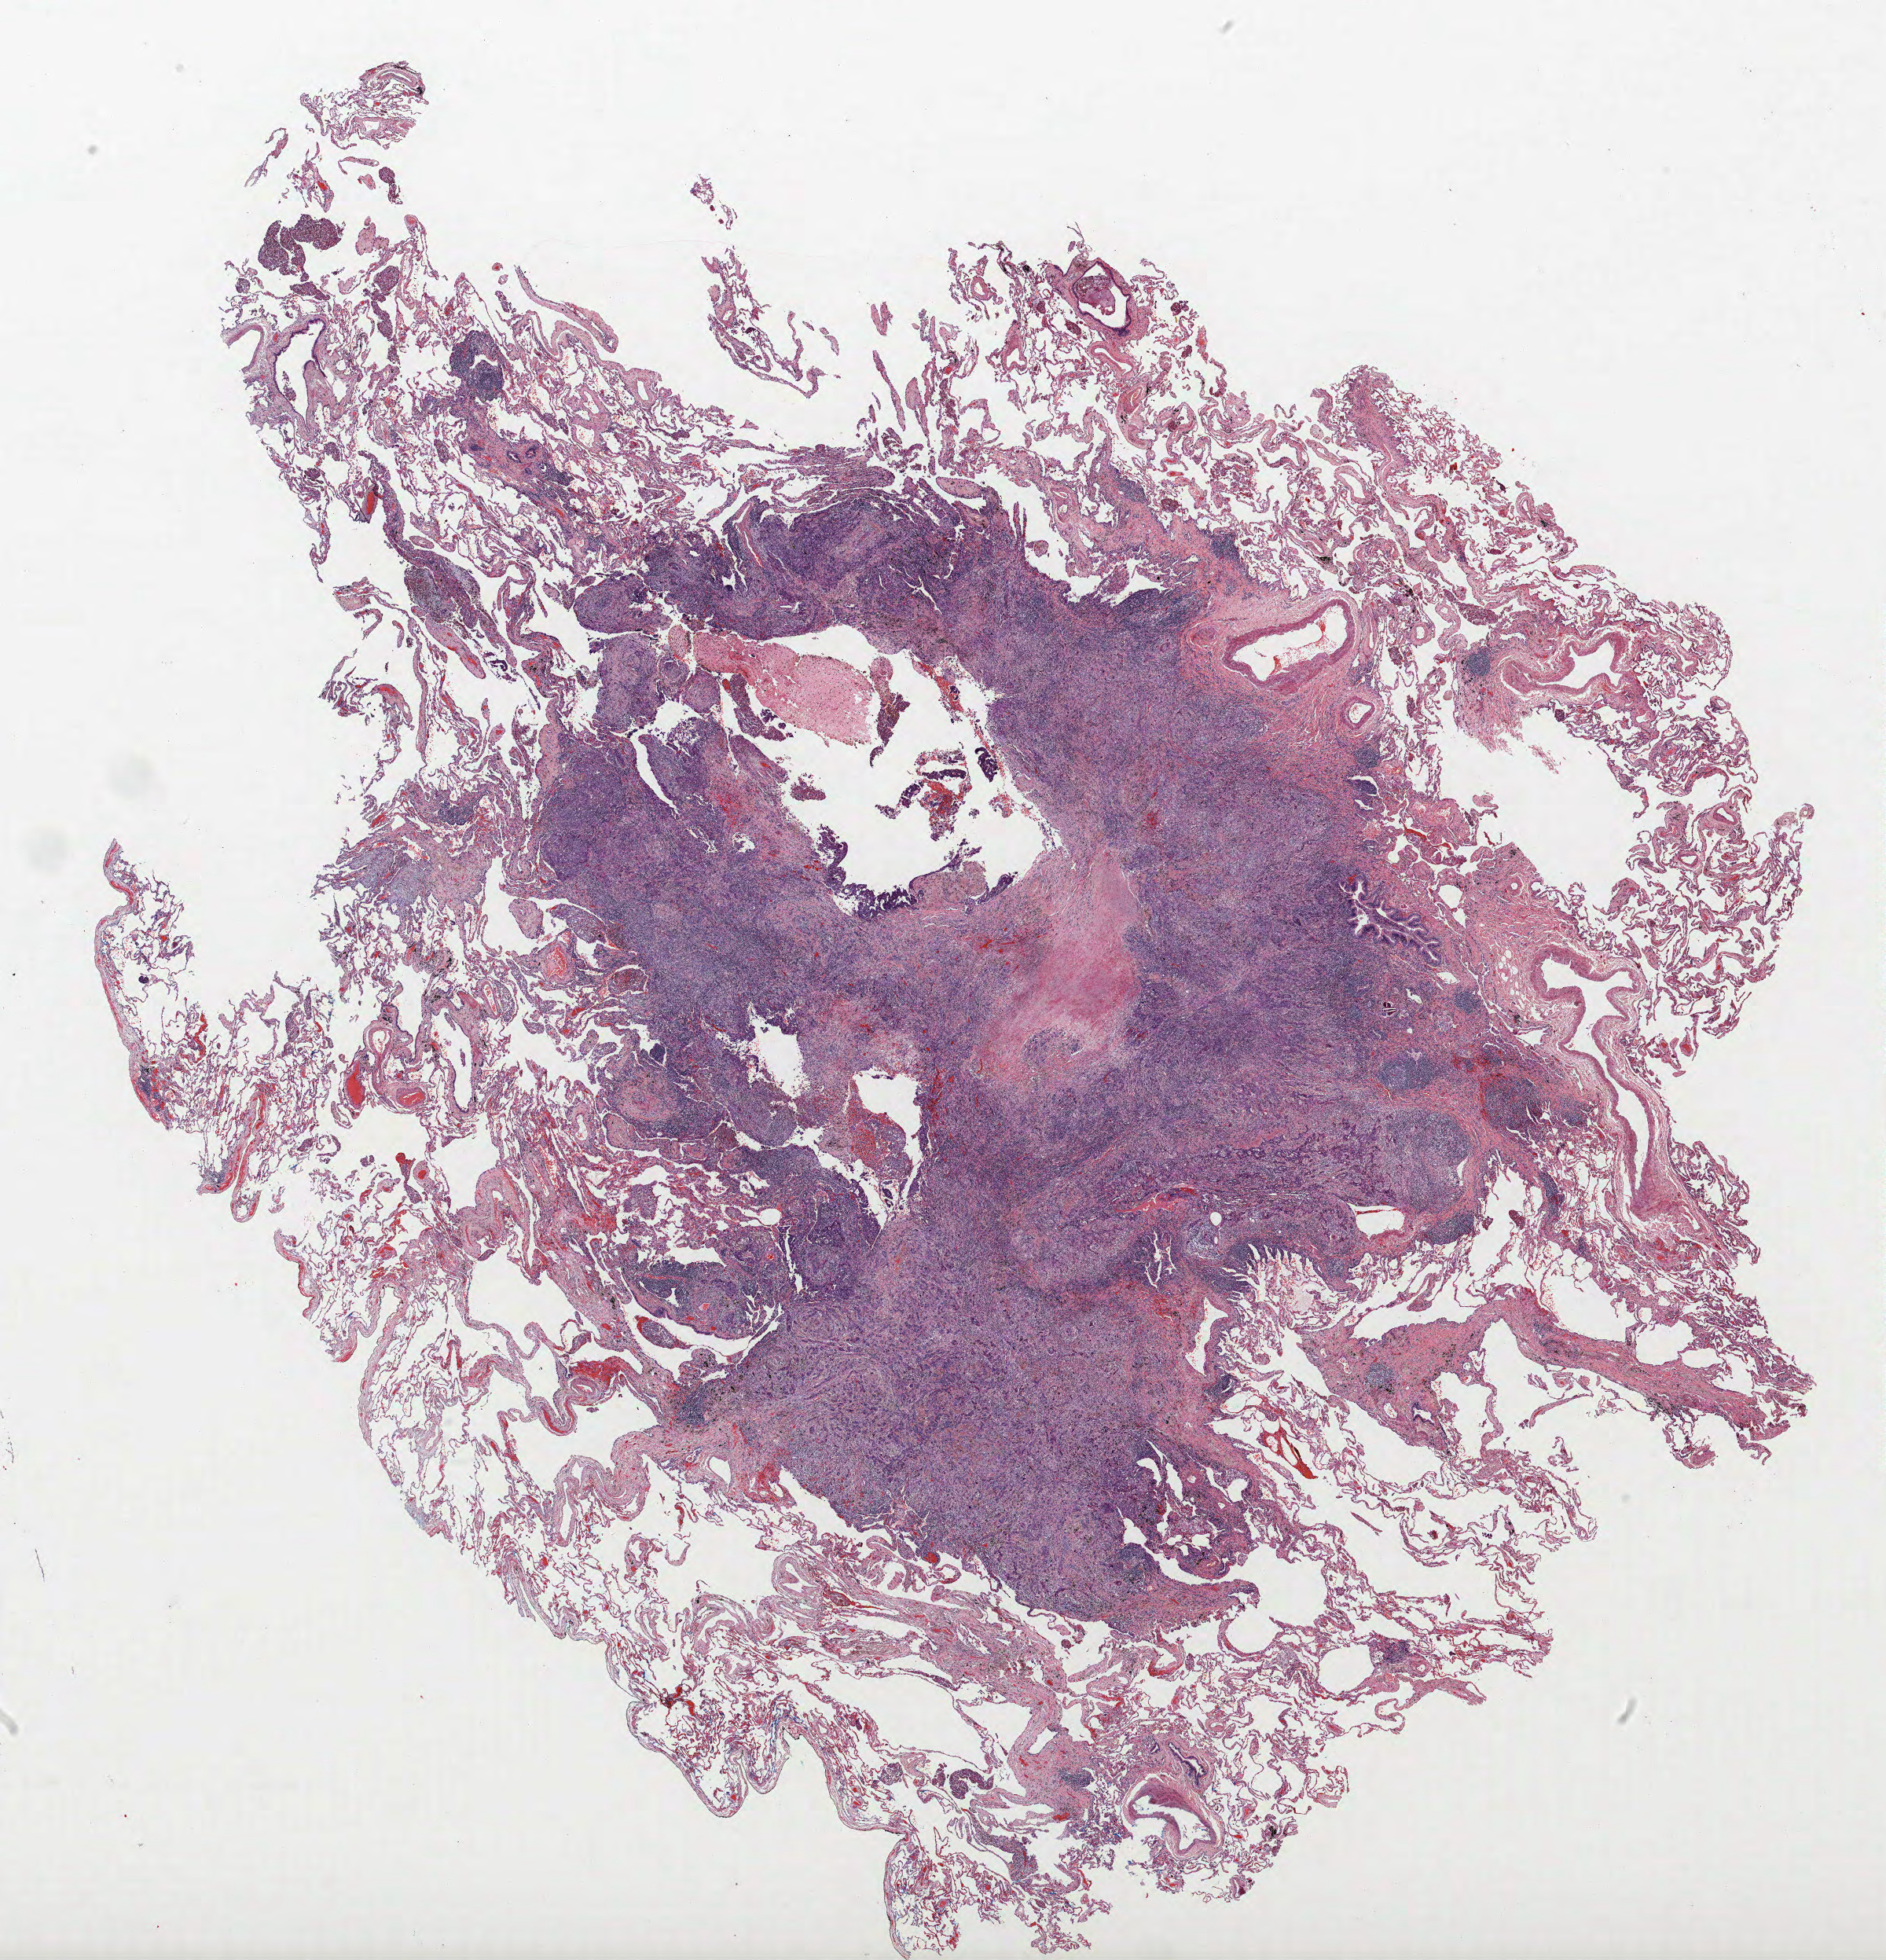
Whole-slide histology image, H&E, shown as a low-resolution overview of the whole scanned area (about 19.2 x 20.0 mm, from a 40x scan). FFPE section. Lung tissue. Female patient, aged 64 at enrolment. Current smoker at enrolment.
Participant's lung-cancer diagnosis: Adenocarcinoma, NOS.